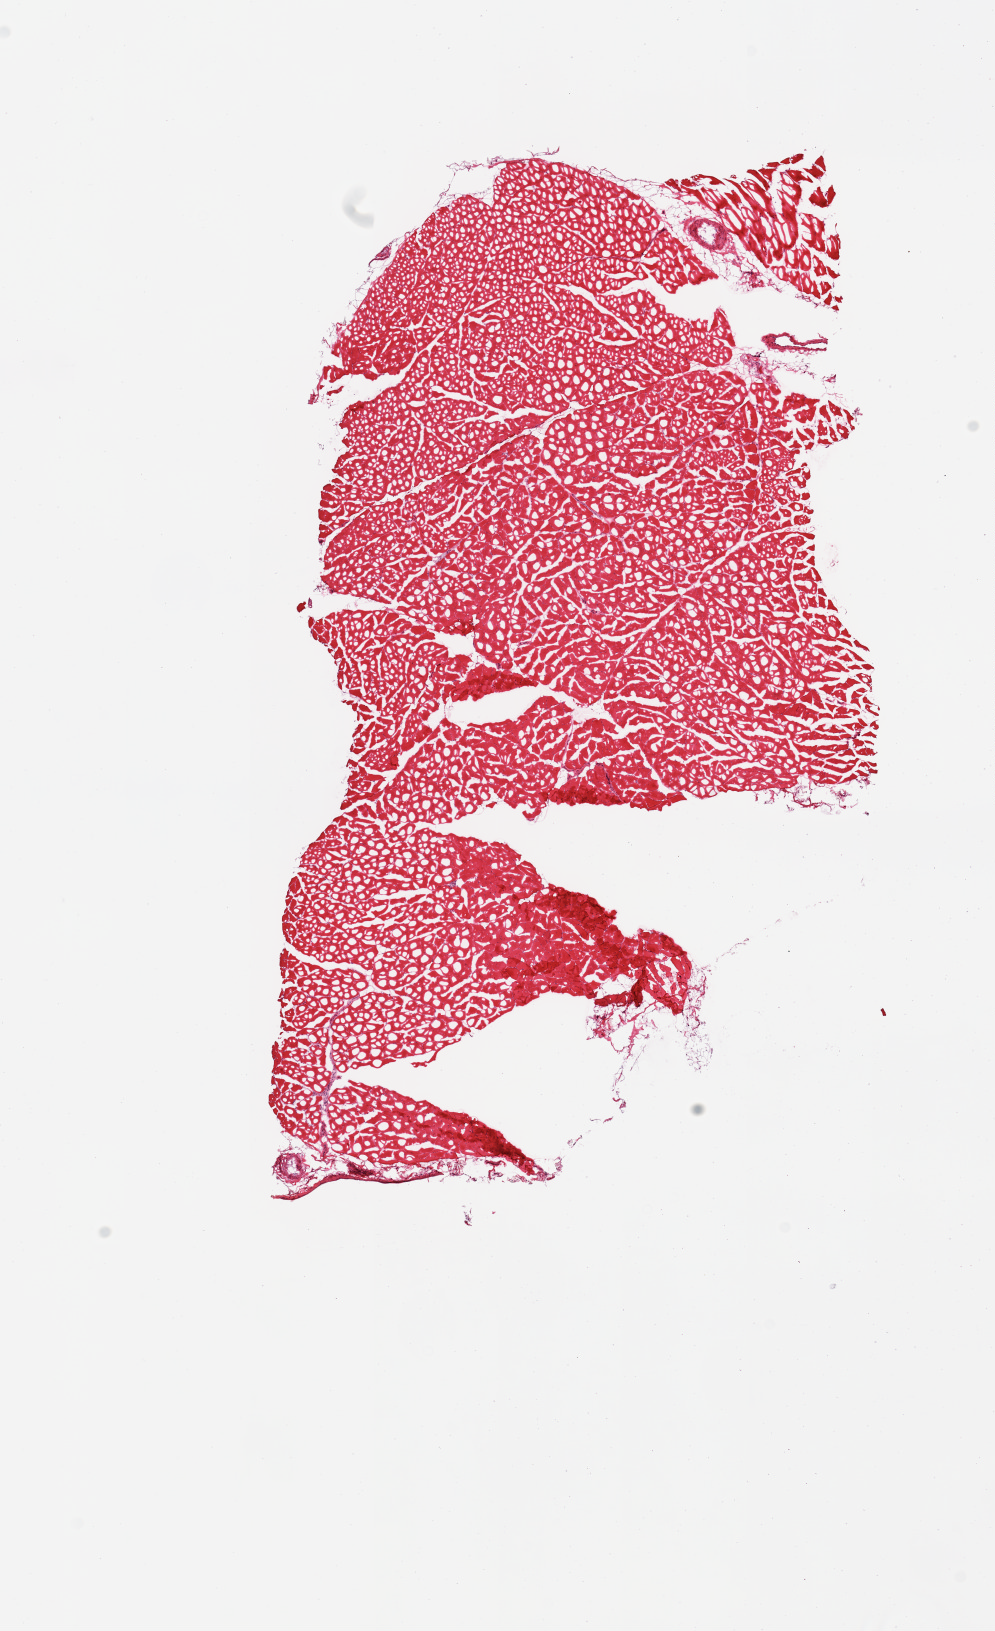
H&E whole-slide image — whole scanned area (about 7.9 x 12.9 mm) shown as a low-resolution overview. Donor sex: female.
* specimen: frozen section; target tissue: skeletal muscle; donor tissue sample